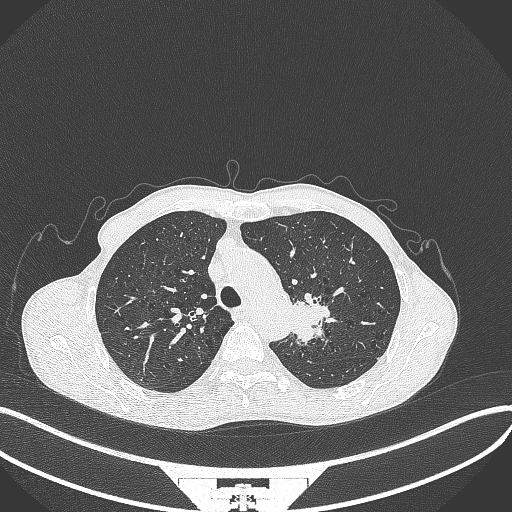
Chest CT, one axial slice. Position 311 of 386 along the scan axis. 120 kVp. Lung window (W 1500 / L -600 HU). 512 × 512 image matrix, field of view 400 × 400 mm. Patient: male, 65 years. From the clinical record (not read from this slice): clinical TNM (as recorded): T2b N0 M0; histopathological grade: G2.
Annotated regions visible in this slice (rectangle marked by the reading radiologist):
- lung tumour (recorded histology: adenocarcinoma): bounding box [x1, y1, x2, y2] px = [289, 292, 333, 343]